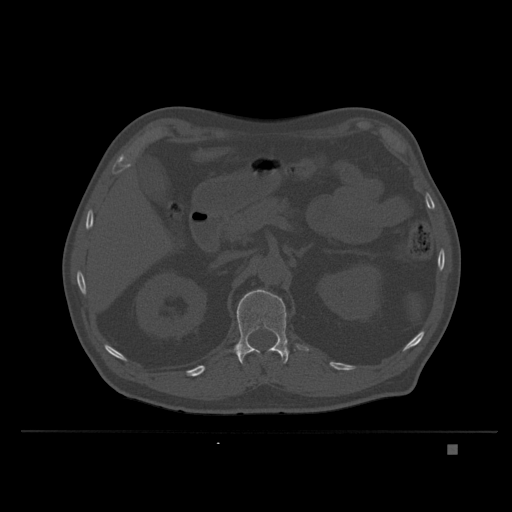
CT including the spine, one axial slice. Position 142 of 435 along the scan axis. Bone window (W 1800 / L 400 HU). 1.5 mm slice thickness. 512 × 512 image matrix, field of view 434 × 434 mm. Male patient, age 73 years. From the clinical record (not read from this slice): primary cancer: skin.
Annotated regions visible in this slice (semi-automatically segmented with operator editing):
- L1 vertebra: box from (x=235, y=289) to (x=309, y=365) px
- T12 vertebra: (x=250, y=350)–(x=254, y=353)